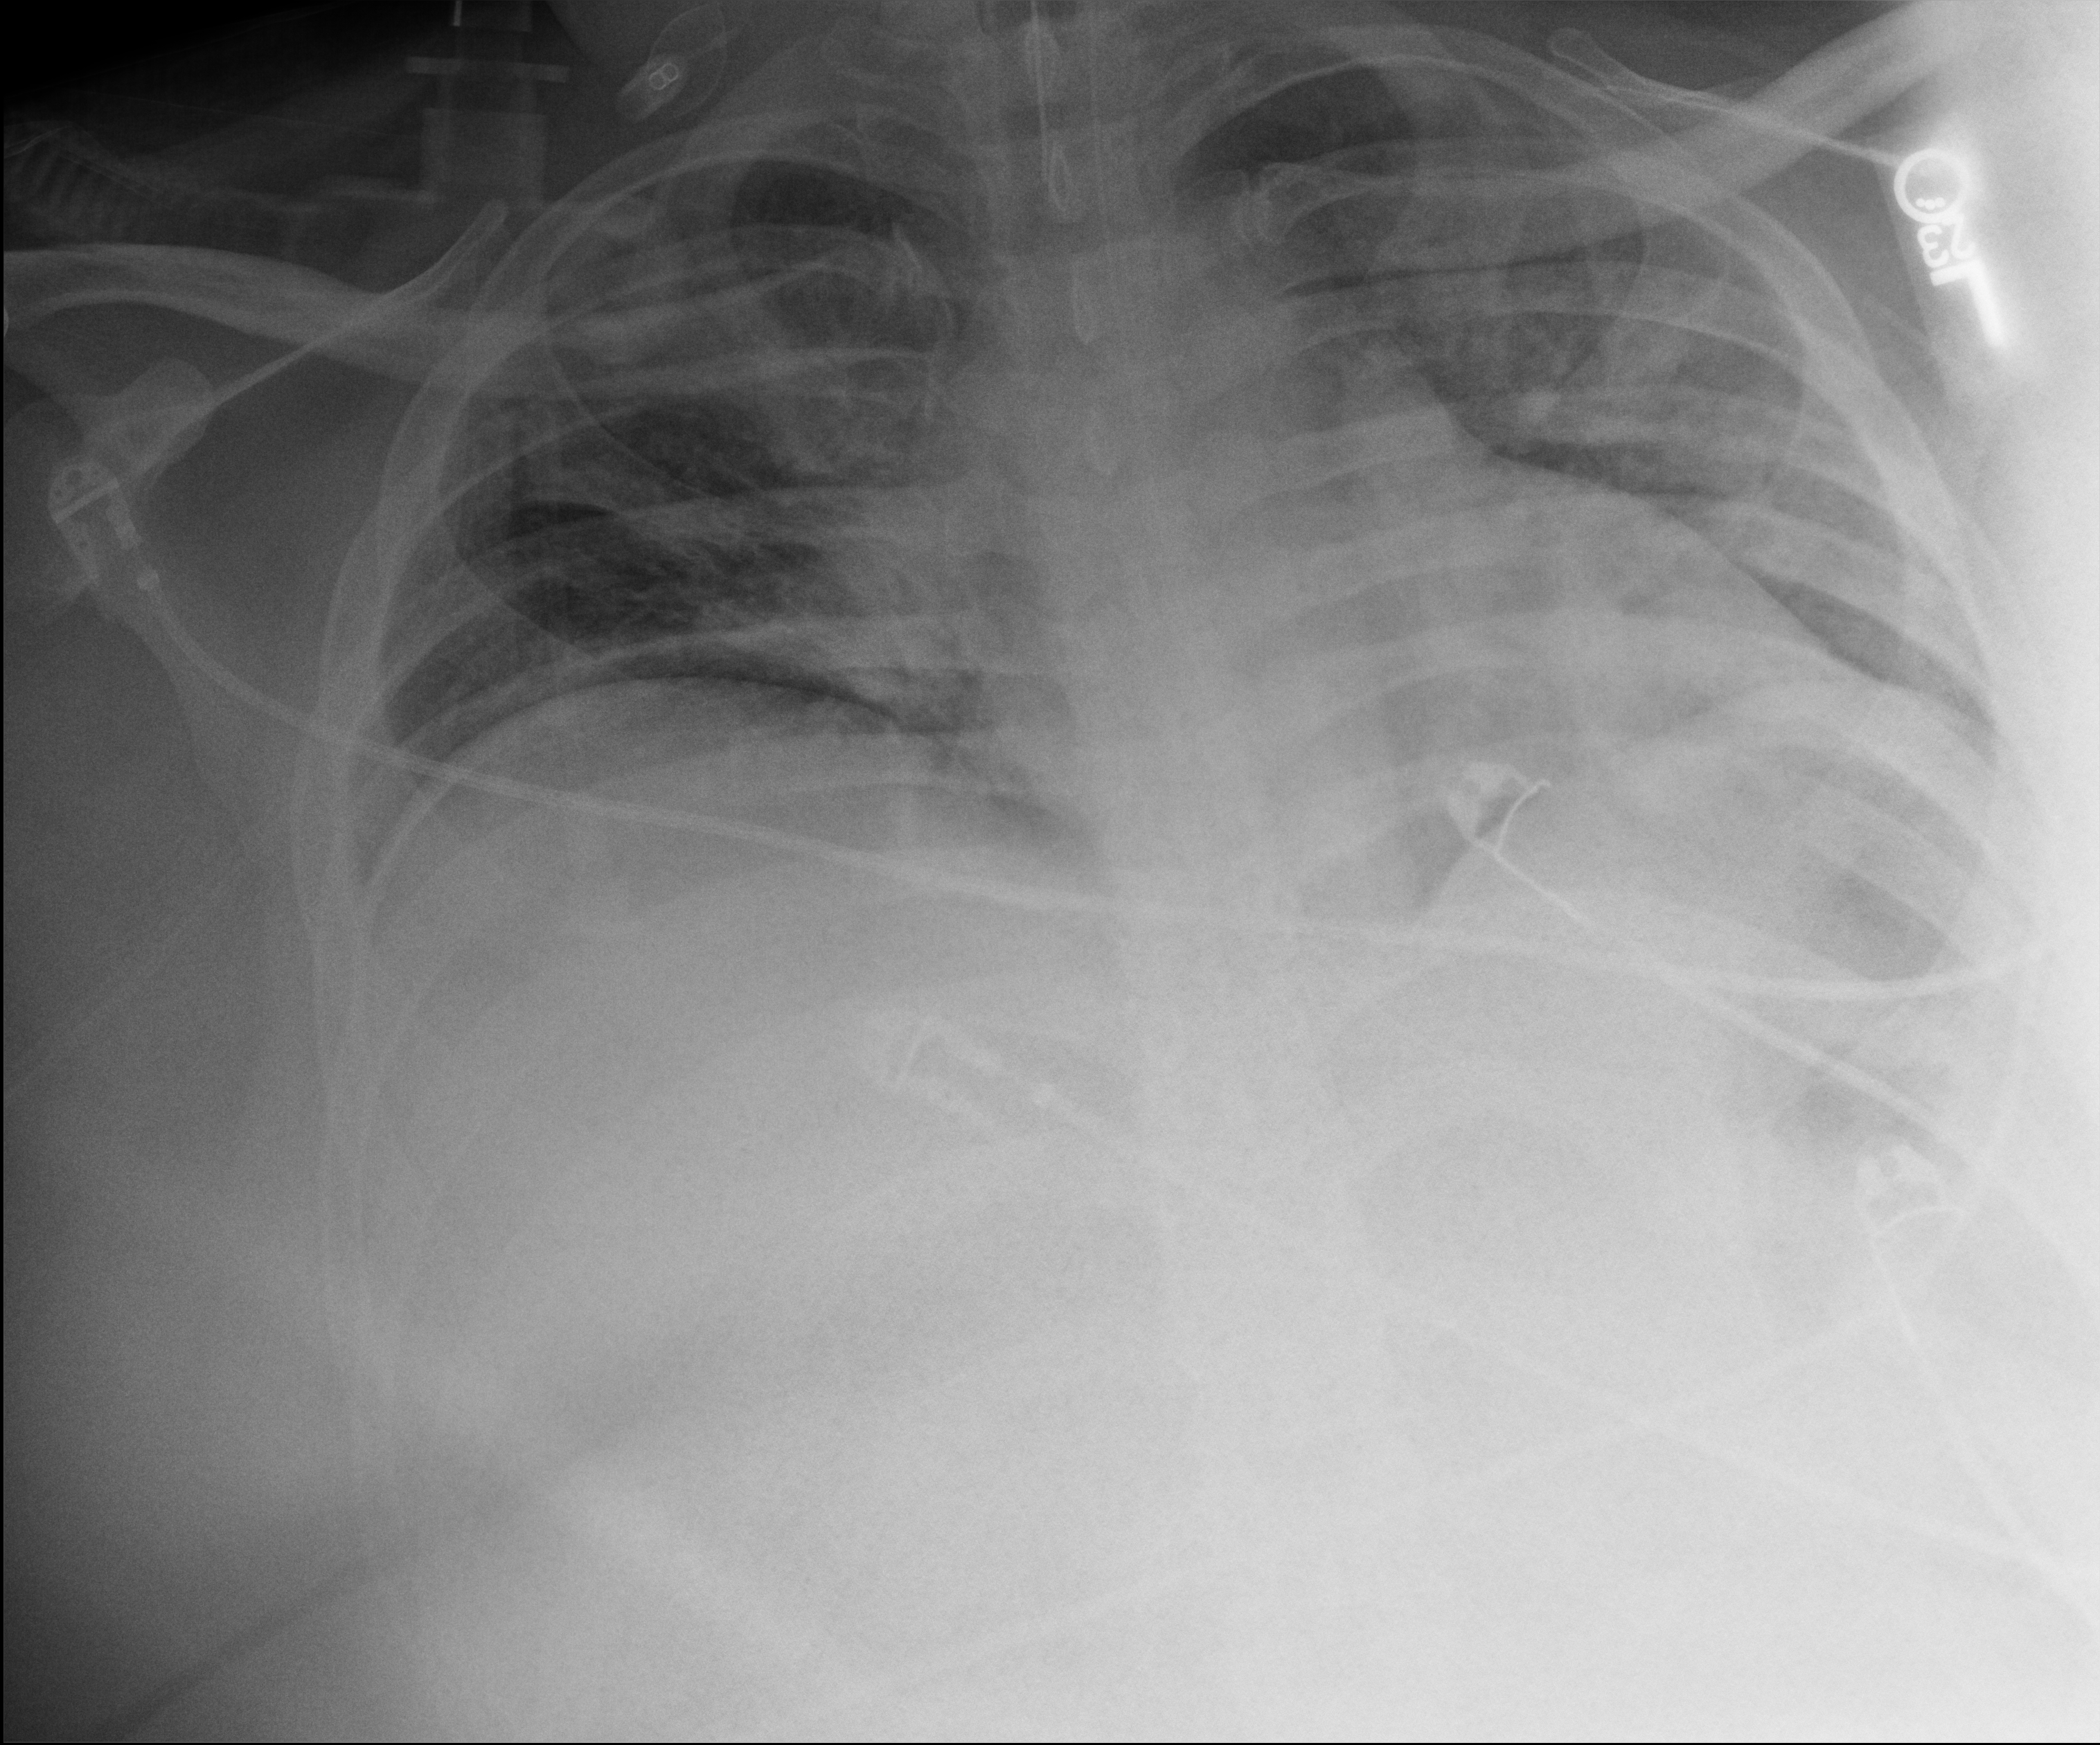
Bedside chest radiograph (digital radiography), anteroposterior (AP) projection. Patient hospitalised with COVID-19; male, aged 18–59 years.
Admission-level facts for this patient (not findings on this image; timing relative to this image not recorded): admitted to intensive care during this hospital stay: yes; smoking status (admission record): never; mechanically ventilated during this hospital stay: yes.